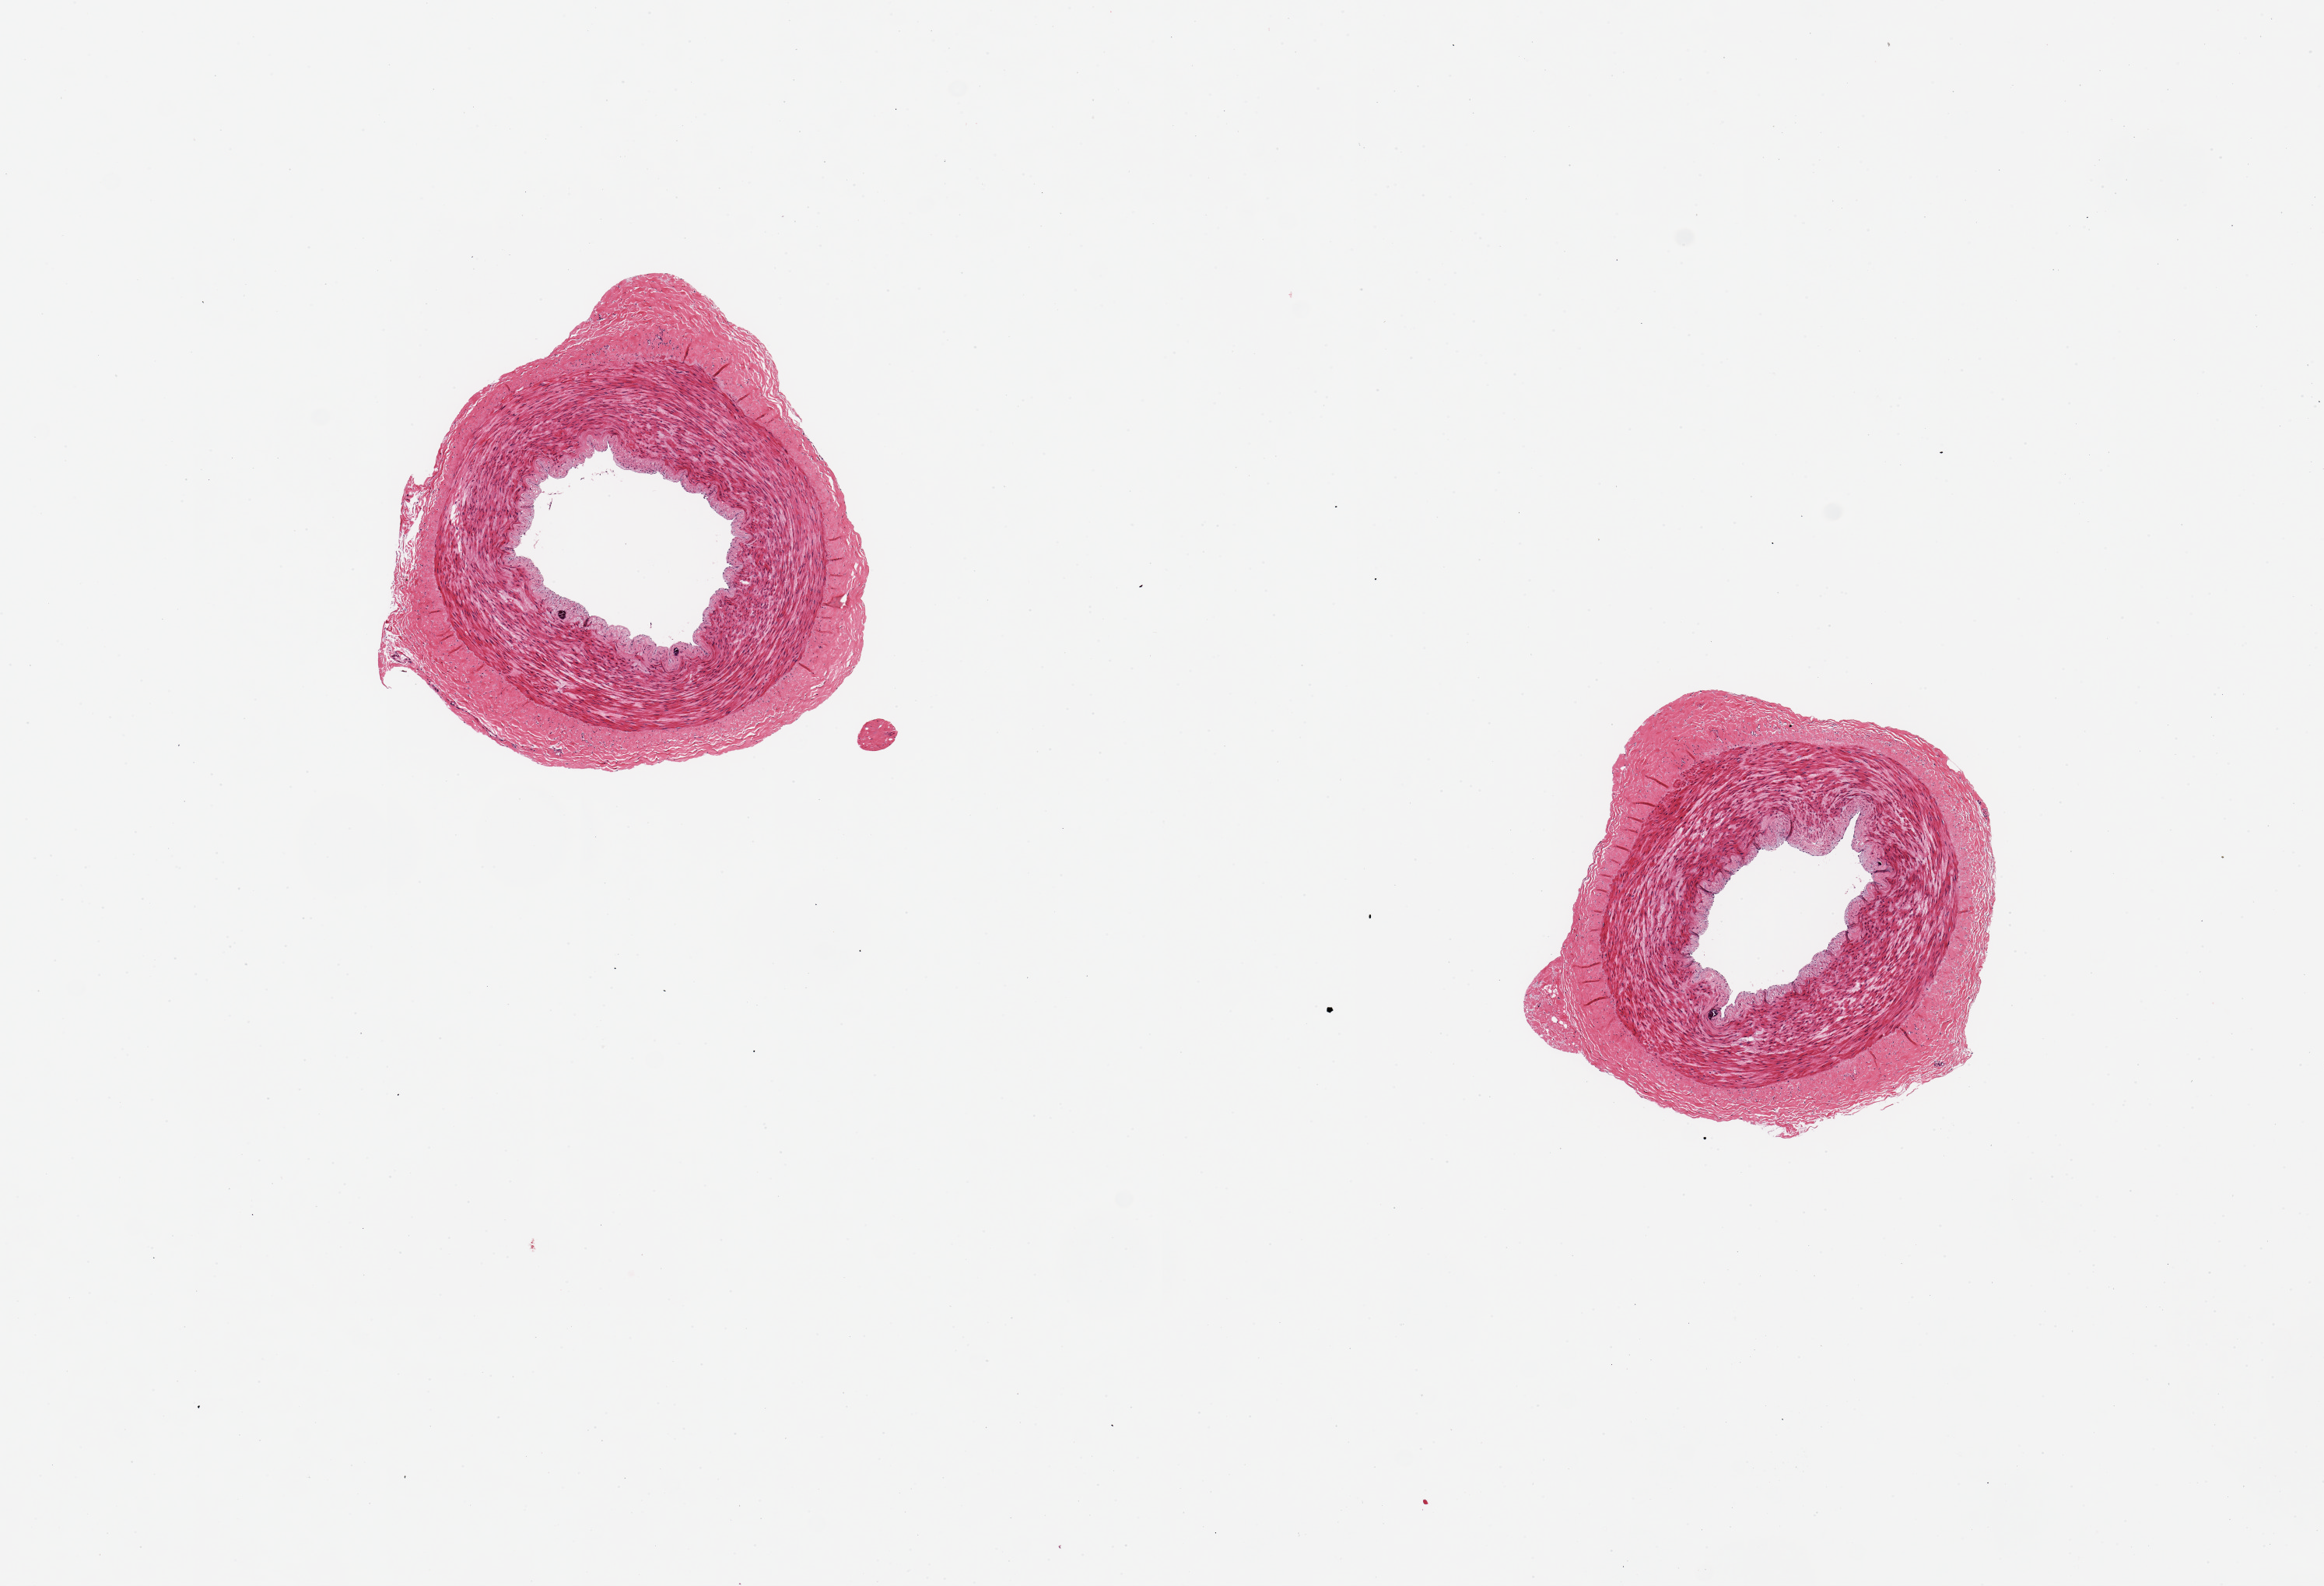
Whole-slide image, haematoxylin and eosin stain, whole scanned area (about 11.8 x 8.1 mm, slide scanned at 20x) shown as a low-resolution overview; PAXgene-fixed, paraffin-embedded tissue; target tissue: tibial artery; donor tissue sample. Donor sex: male.
Reviewer comment on this tissue sample: 2 pieces ,2 mm artery; a few punctate calcium deposits in intima; clean, no adipose.